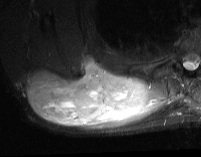
MRI of an extremity soft-tissue mass, one axial slice. Slice 27 of 74 in the series (ordered by position). STIR. MR volume resampled by the dataset authors to the PET/CT grid (not the native acquisition matrix). 3.27 mm slice thickness. 201 × 157 image matrix, field of view 196 × 153 mm. Male patient. Case-level facts recorded for this patient, not image findings: histological type: pleiomorphic spindle cell undifferentiated; grade: high; site of the primary tumour: right parascapusular.
Annotated regions visible in this slice (expert contour drawn on MRI and transferred to this co-registered scan by the dataset authors):
- gross tumour volume including surrounding oedema: box from (x=26, y=59) to (x=168, y=129) px
- gross tumour volume (mass): (x=26, y=59)–(x=150, y=126)